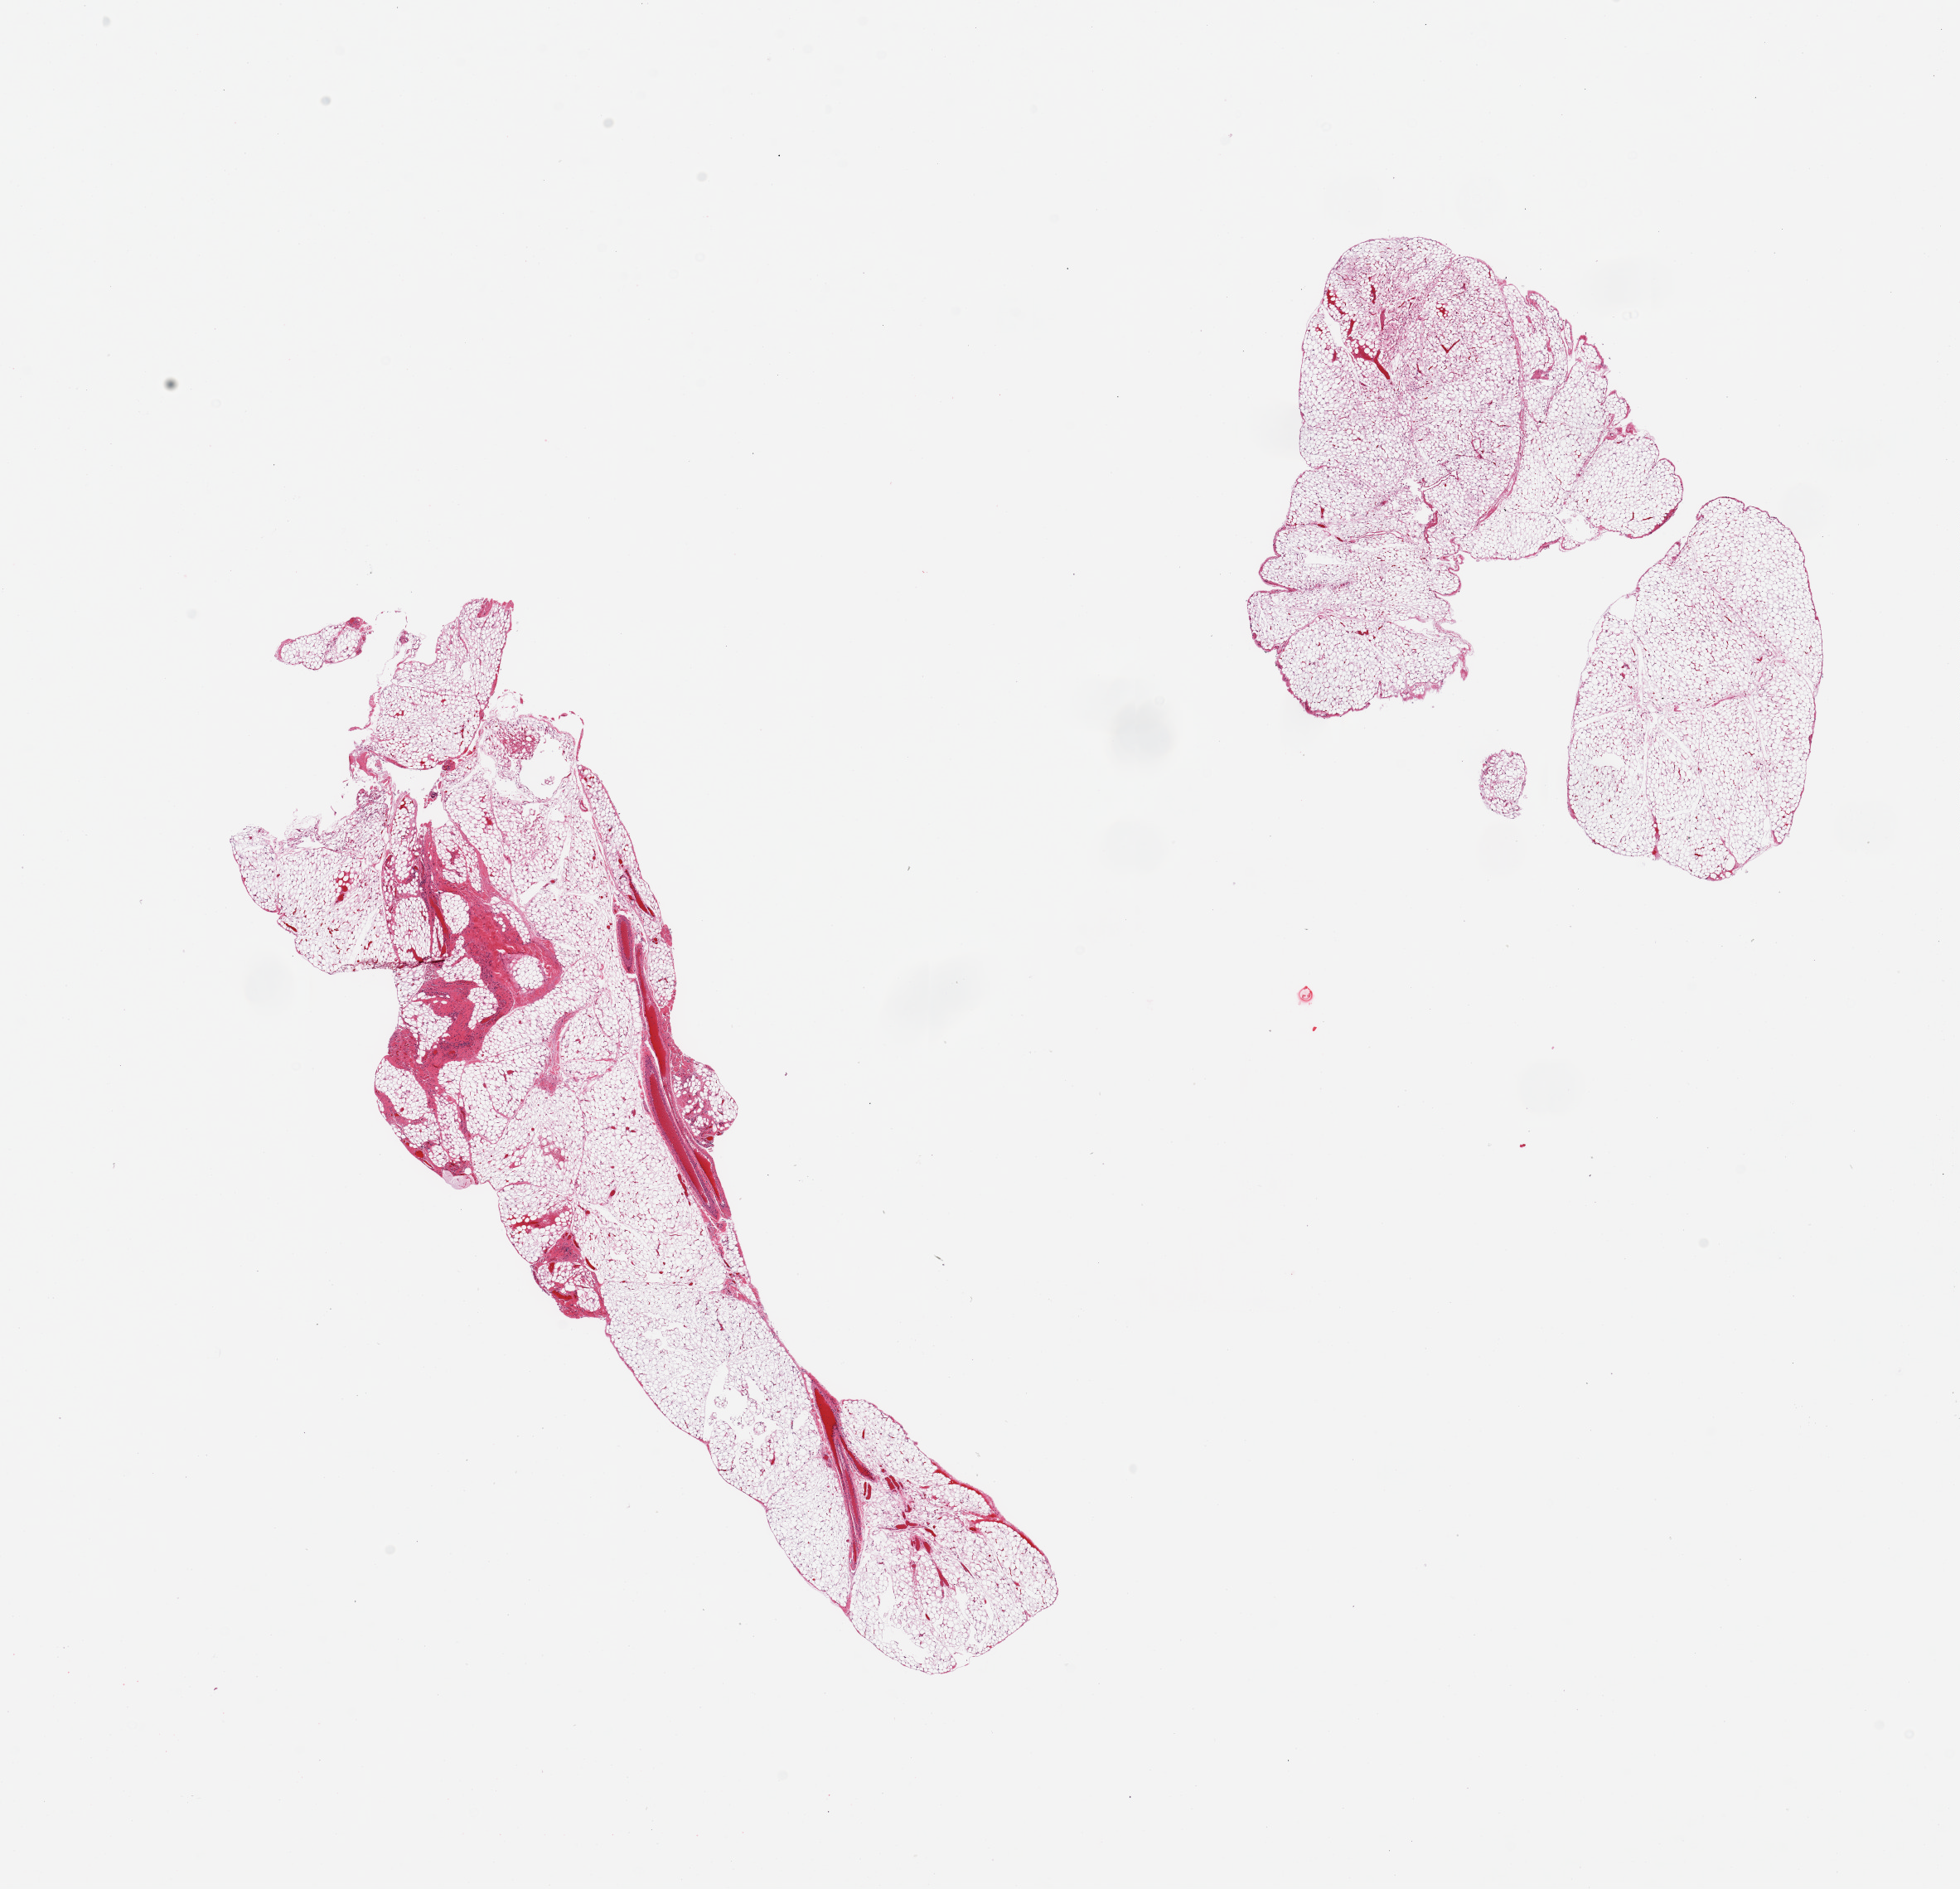
H&E whole-slide image, a low-resolution overview of the entire scanned area, about 18.7 x 18.0 mm (from a 20x scan); PAXgene-fixed, paraffin-embedded tissue; sampled site (target tissue): omentum; donor tissue sample. Donor: male.
Review note (as recorded): 2 pieces; 1 piece with 10% fibrovascular content, other with <1% such content.